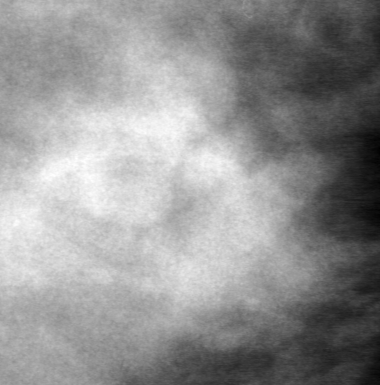
Region of interest cut from a scanned film mammogram (one marked finding); left breast; MLO view; BI-RADS breast density category 3 (scale 1–4).
Mass, shape lobulated, margins microlobulated; BI-RADS assessment category 0 (incomplete: needs additional imaging); subtlety rating 3 on a 1 (subtle) to 5 (obvious) scale; pathology (as recorded): benign.